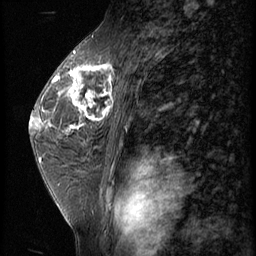
Breast MRI (dynamic contrast-enhanced), one sagittal slice; slice 36 of 62 in the series (ordered by position); 3 images stored at this slice position (order not interpretable as contrast timing); 1.5 T; TE 4.2 ms, TR 9 ms; 2.5 mm slice thickness; 256 × 256 image matrix, field of view 180 × 180 mm. Female patient, age 44 years. From the clinical record (not read from this slice): setting: breast cancer imaged before/during neoadjuvant chemotherapy; receptor status: triple-negative.
Structures marked on this image (semi-automatic segmentation, software-assisted and operator-edited):
- analysis volume of interest (the breast-tissue region the enhancement analysis was run in; not a lesion): bounding box <67,64,116,125> (left, top, right, bottom; pixels)
- tumour enhancement mask (voxels above the 140 % enhancement threshold inside the analysis volume of interest): <67,64,116,122>